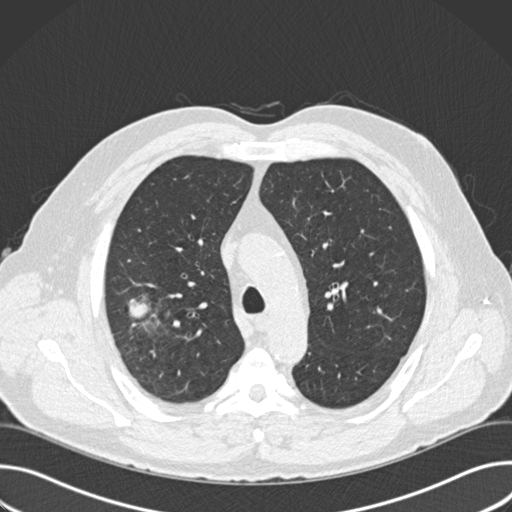
Low-dose screening chest CT, one axial slice; position 116 of 157 along the scan axis; lung window (W 1500 / L -600 HU); 2 mm slice thickness; 512 × 512 image matrix, field of view 380 × 380 mm.
Annotated regions visible in this slice (manually delineated by an expert):
- lesion 1 (tumor, upper lobe of right lung): bounding box [x1, y1, x2, y2] px = [129, 299, 150, 318]